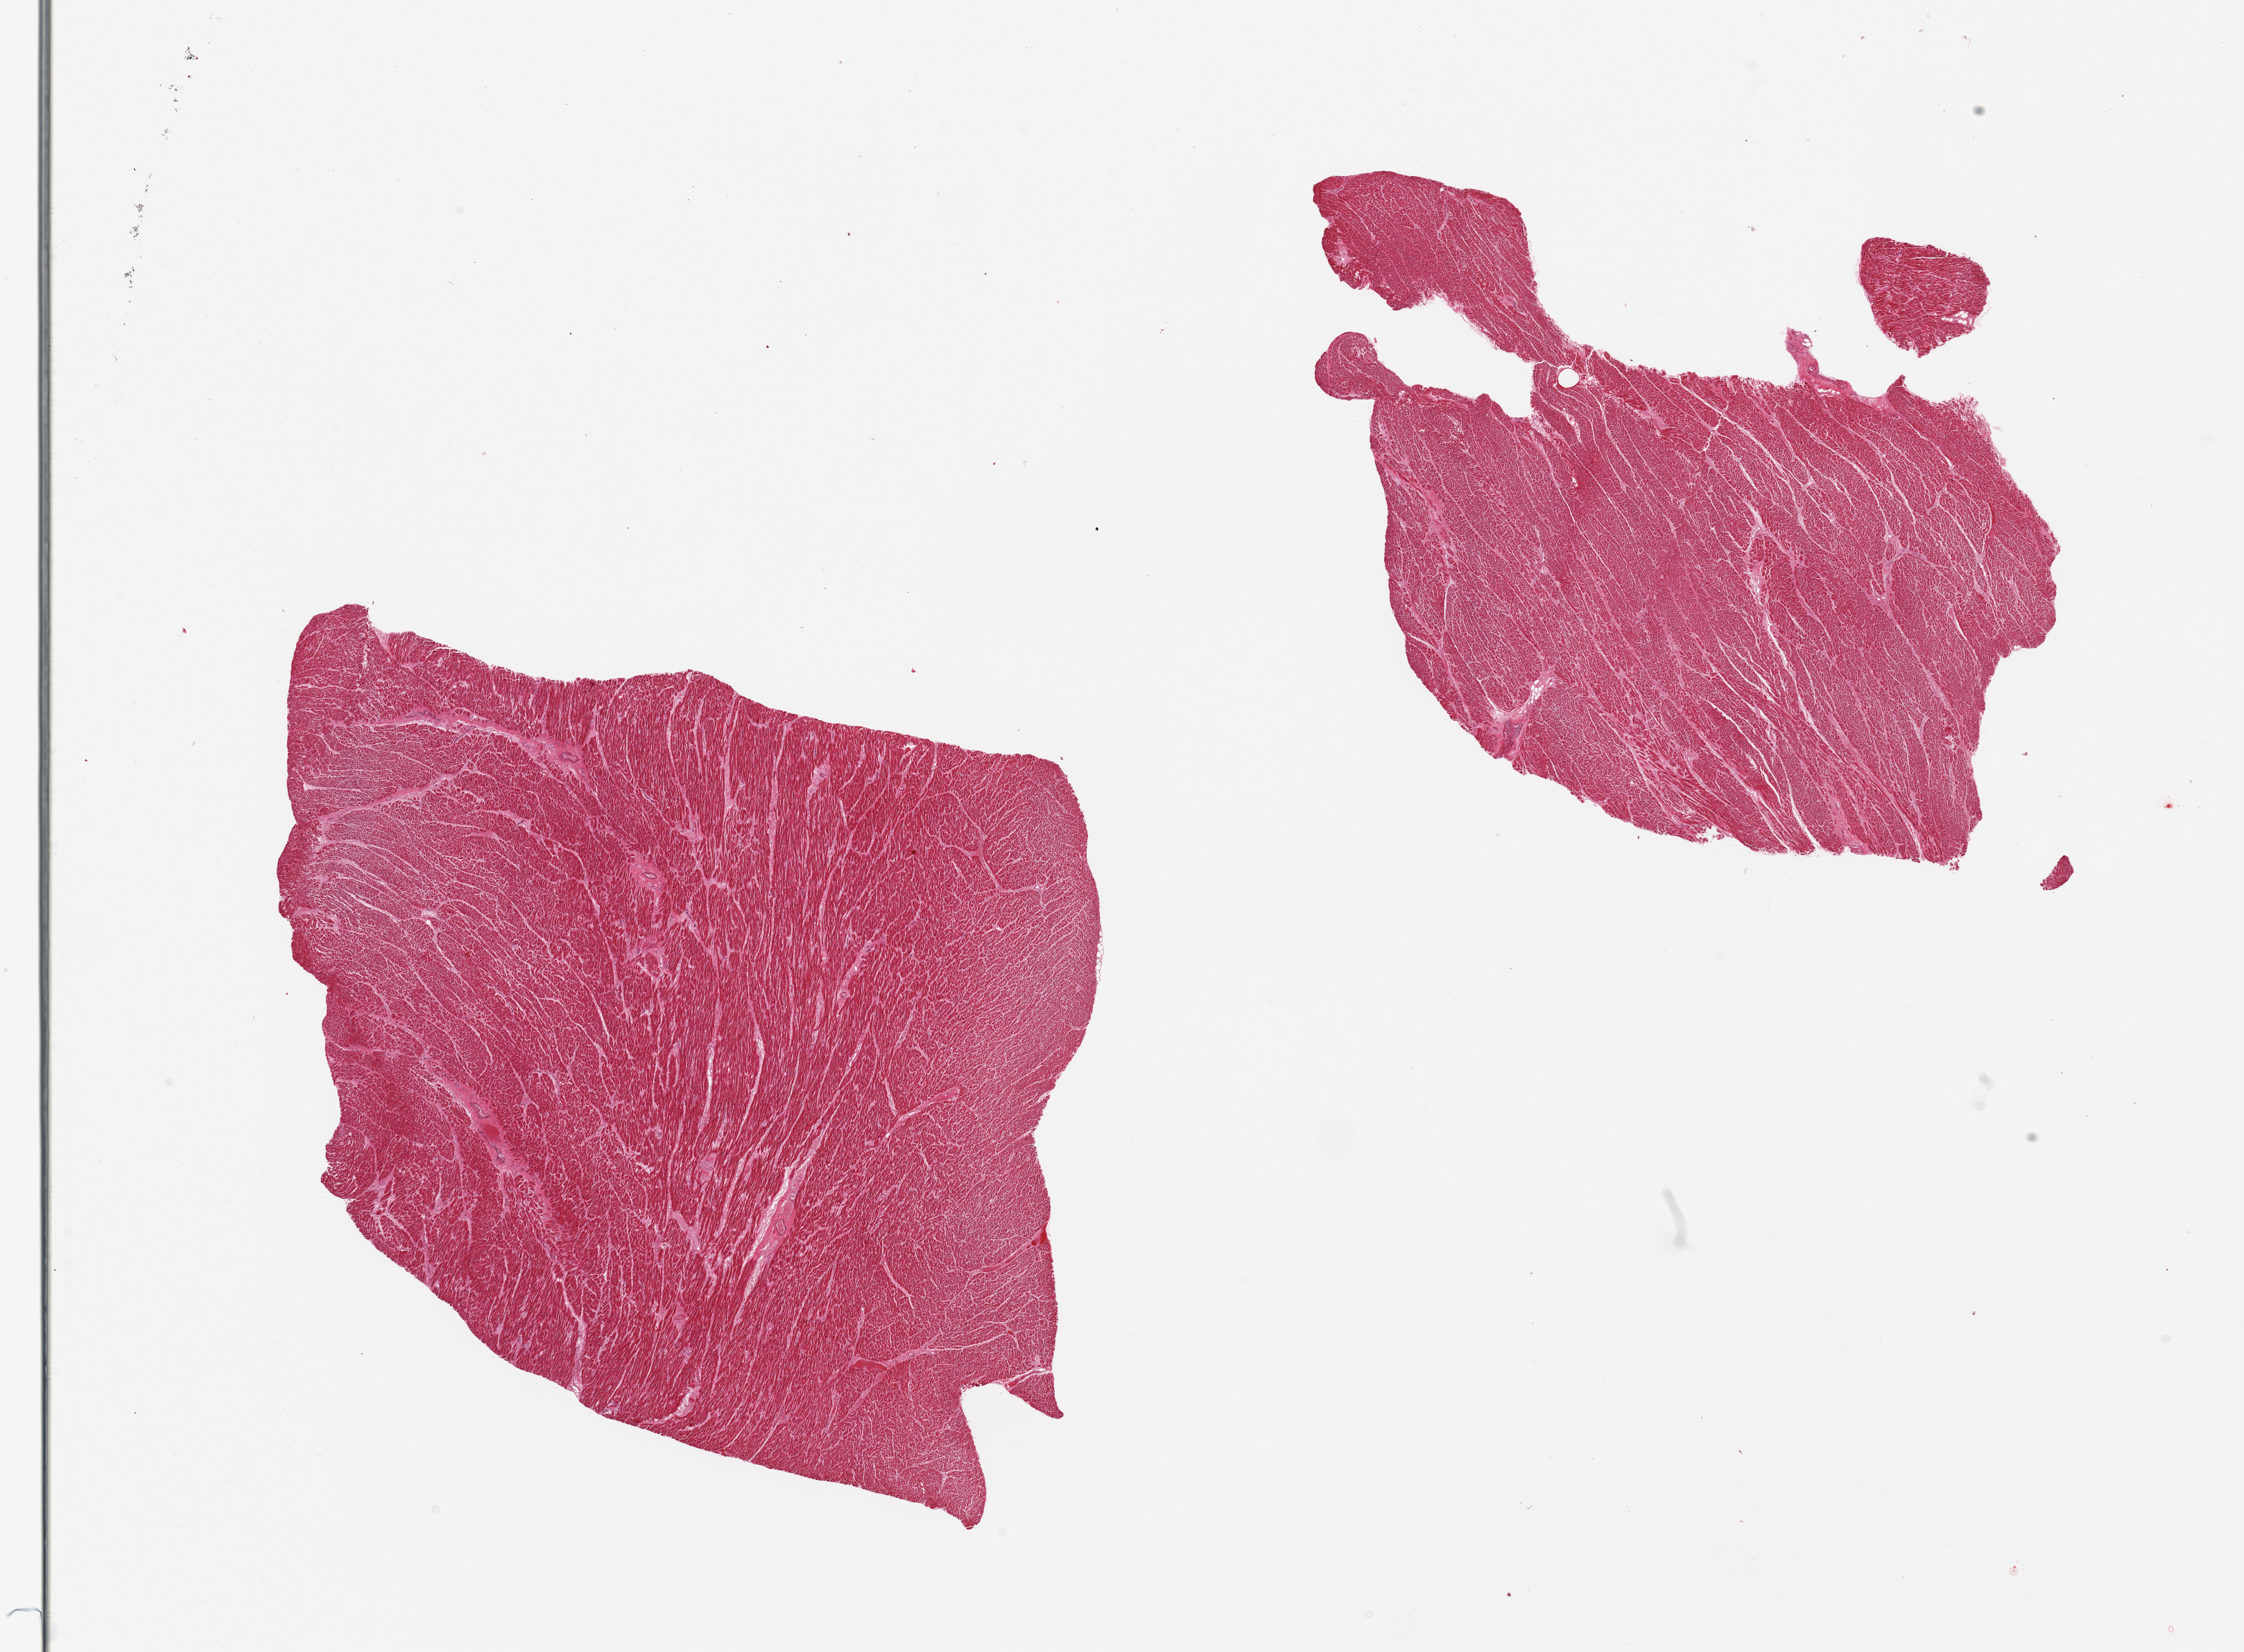
H&E whole-slide image — whole scanned area (about 25.6 x 18.8 mm) shown as a low-resolution overview; PAXgene-fixed, paraffin-embedded tissue; sampled site (target tissue): heart; tissue donor sample. Male donor.
* reviewer comment on this tissue sample: 2 pieces, minimal ischemic damage/interstitial fibrosis